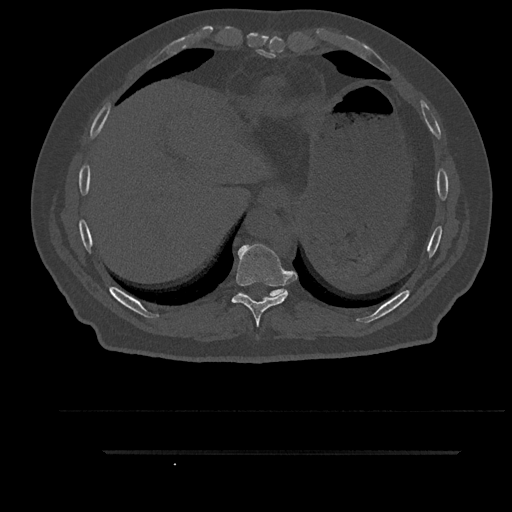
CT including the spine, one axial slice. Position 414 of 797 along the scan axis. Reconstruction kernel Br40s/3. 120 kVp. Bone window (W 1800 / L 400 HU). 512 × 512 image matrix, field of view 432 × 432 mm. Male patient, age 63 years. From the clinical record (not read from this slice): primary cancer: renal; vertebrae with lytic lesions (as recorded): T8.
Structures marked on this image (semi-automatic segmentation, software-assisted and operator-edited):
- T10 vertebra: bounding box [x1, y1, x2, y2] px = [239, 289, 286, 297]
- T9 vertebra: [232, 244, 290, 327]